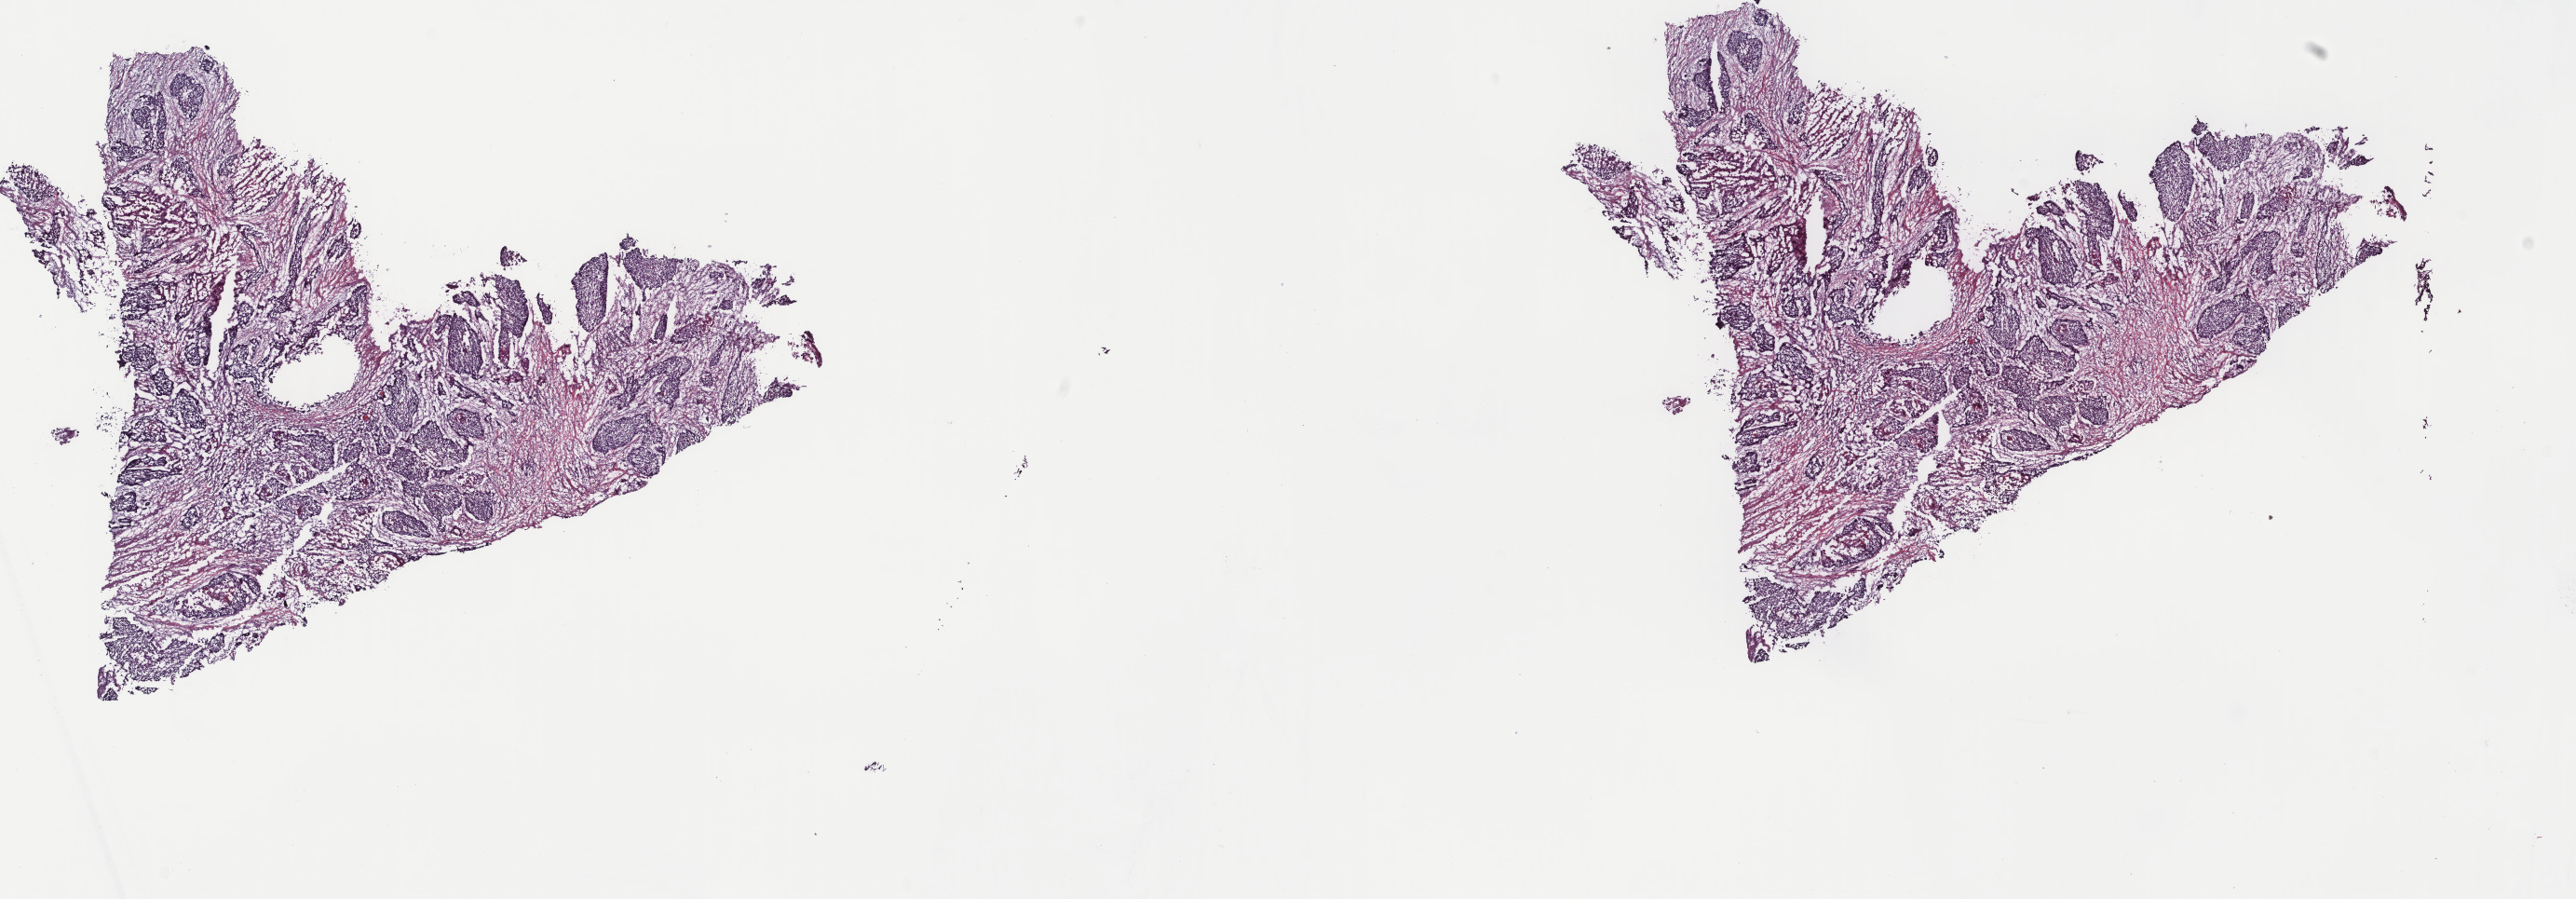
Digitized Hematoxylin and eosin (H&E) stained tissue section (whole slide) — low-resolution overview of the scanned area, about 22.0 x 7.7 mm, frozen section from the top of the tissue portion, primary tumour sample from the esophagus. Patient: male, age at initial diagnosis 57 years. Histologic grade: G1 (well differentiated). Pathologist review of this section (percent, as recorded): tumour cells 70%, tumour nuclei 70%, normal cells 0%, stromal cells 30%, necrosis 0%. Inflammatory infiltration, as recorded: lymphocyte infiltration 4%, monocyte infiltration 2%, neutrophil infiltration 2%.
AJCC pathologic stage: IIA. Histologic diagnosis: Squamous cell carcinoma, NOS.